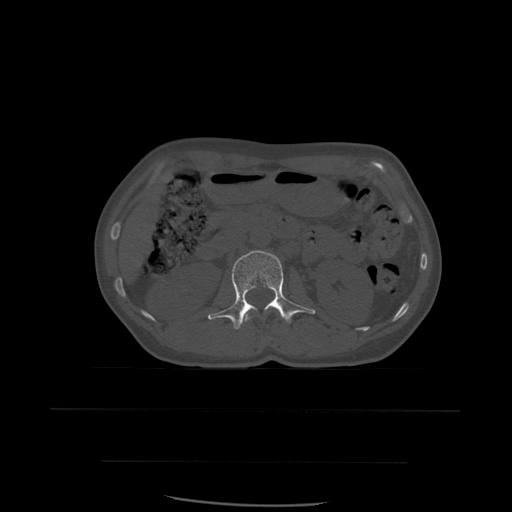
CT including the spine, one axial slice; slice 229 of 574 in the series (ordered by position); bone window (W 1800 / L 400 HU); 512 × 512 image matrix, field of view 392 × 392 mm. Patient age 48 years. From the clinical record (not read from this slice): primary cancer: lung; vertebrae with lytic lesions (as recorded): T11.
Outlined on this slice (semi-automatic segmentation, software-assisted and operator-edited):
- L1 vertebra: bounding box <244,313,278,323> (left, top, right, bottom; pixels)
- L2 vertebra: <208,250,316,330>